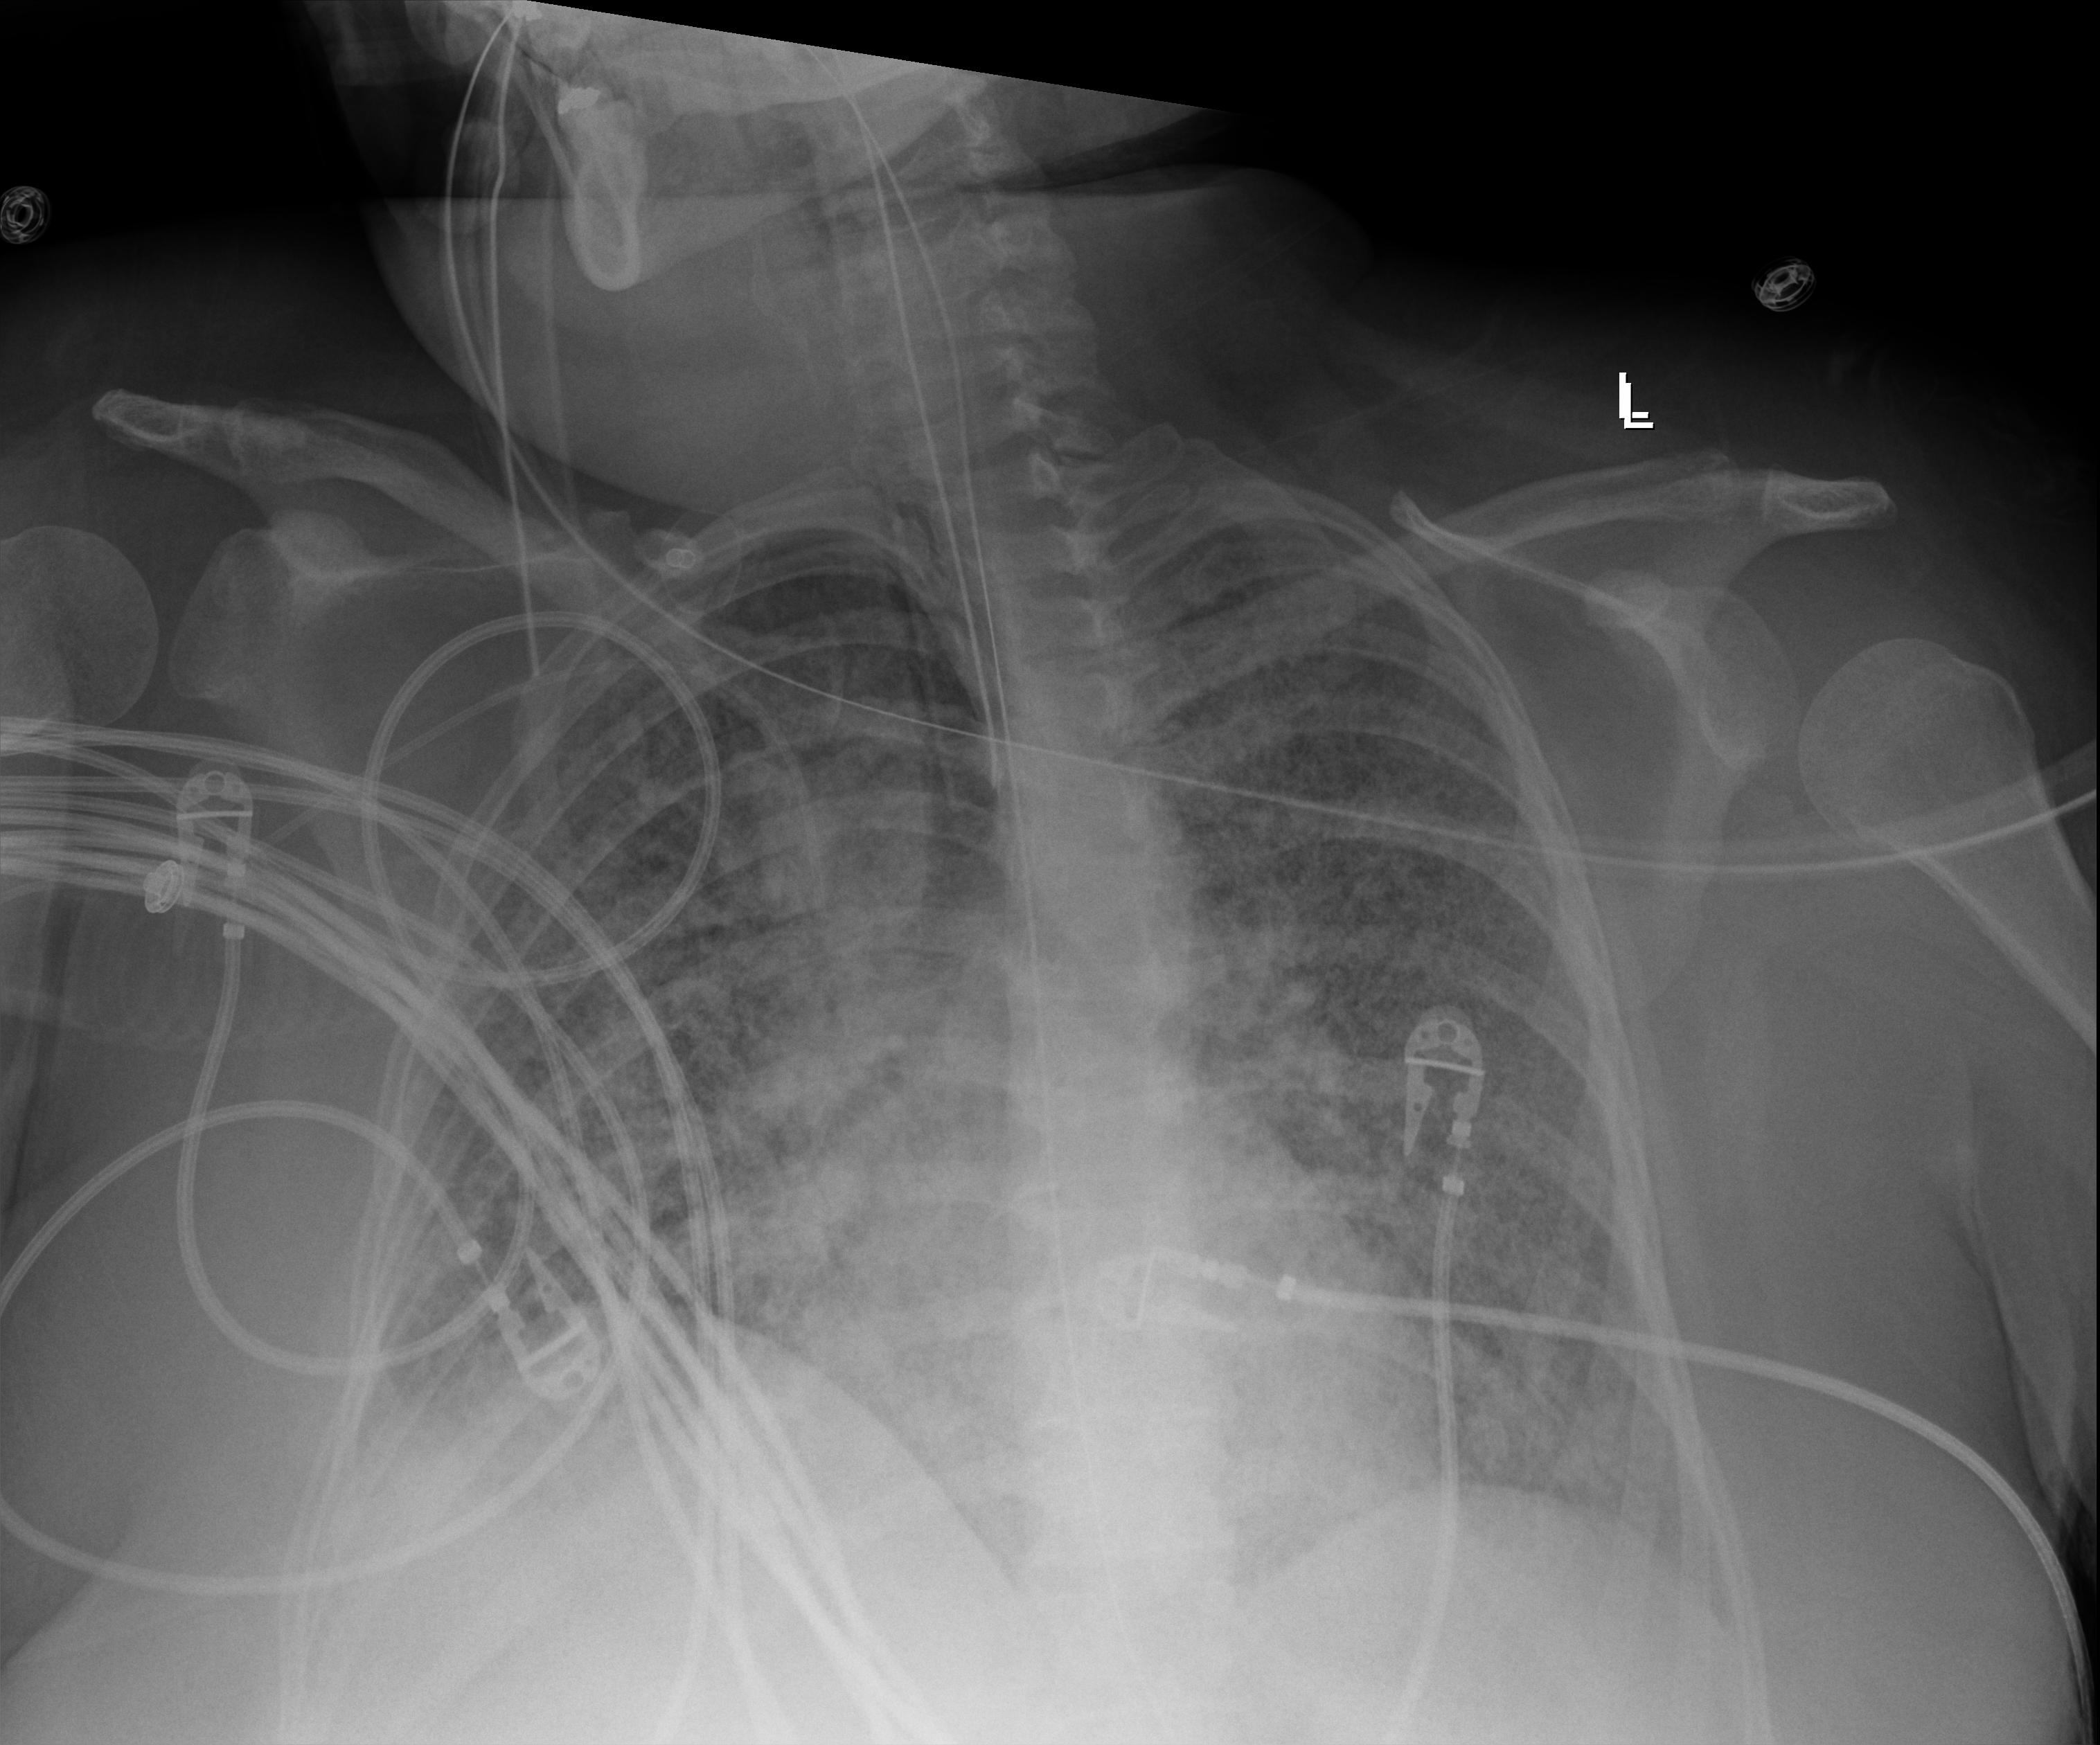
Portable chest radiograph, anteroposterior (AP) projection. Patient hospitalised with COVID-19; female, aged 18–59 years.
From the hospital-stay record, not from the radiograph (when in the stay this image was taken is not recorded): admitted to intensive care during this hospital stay: yes.